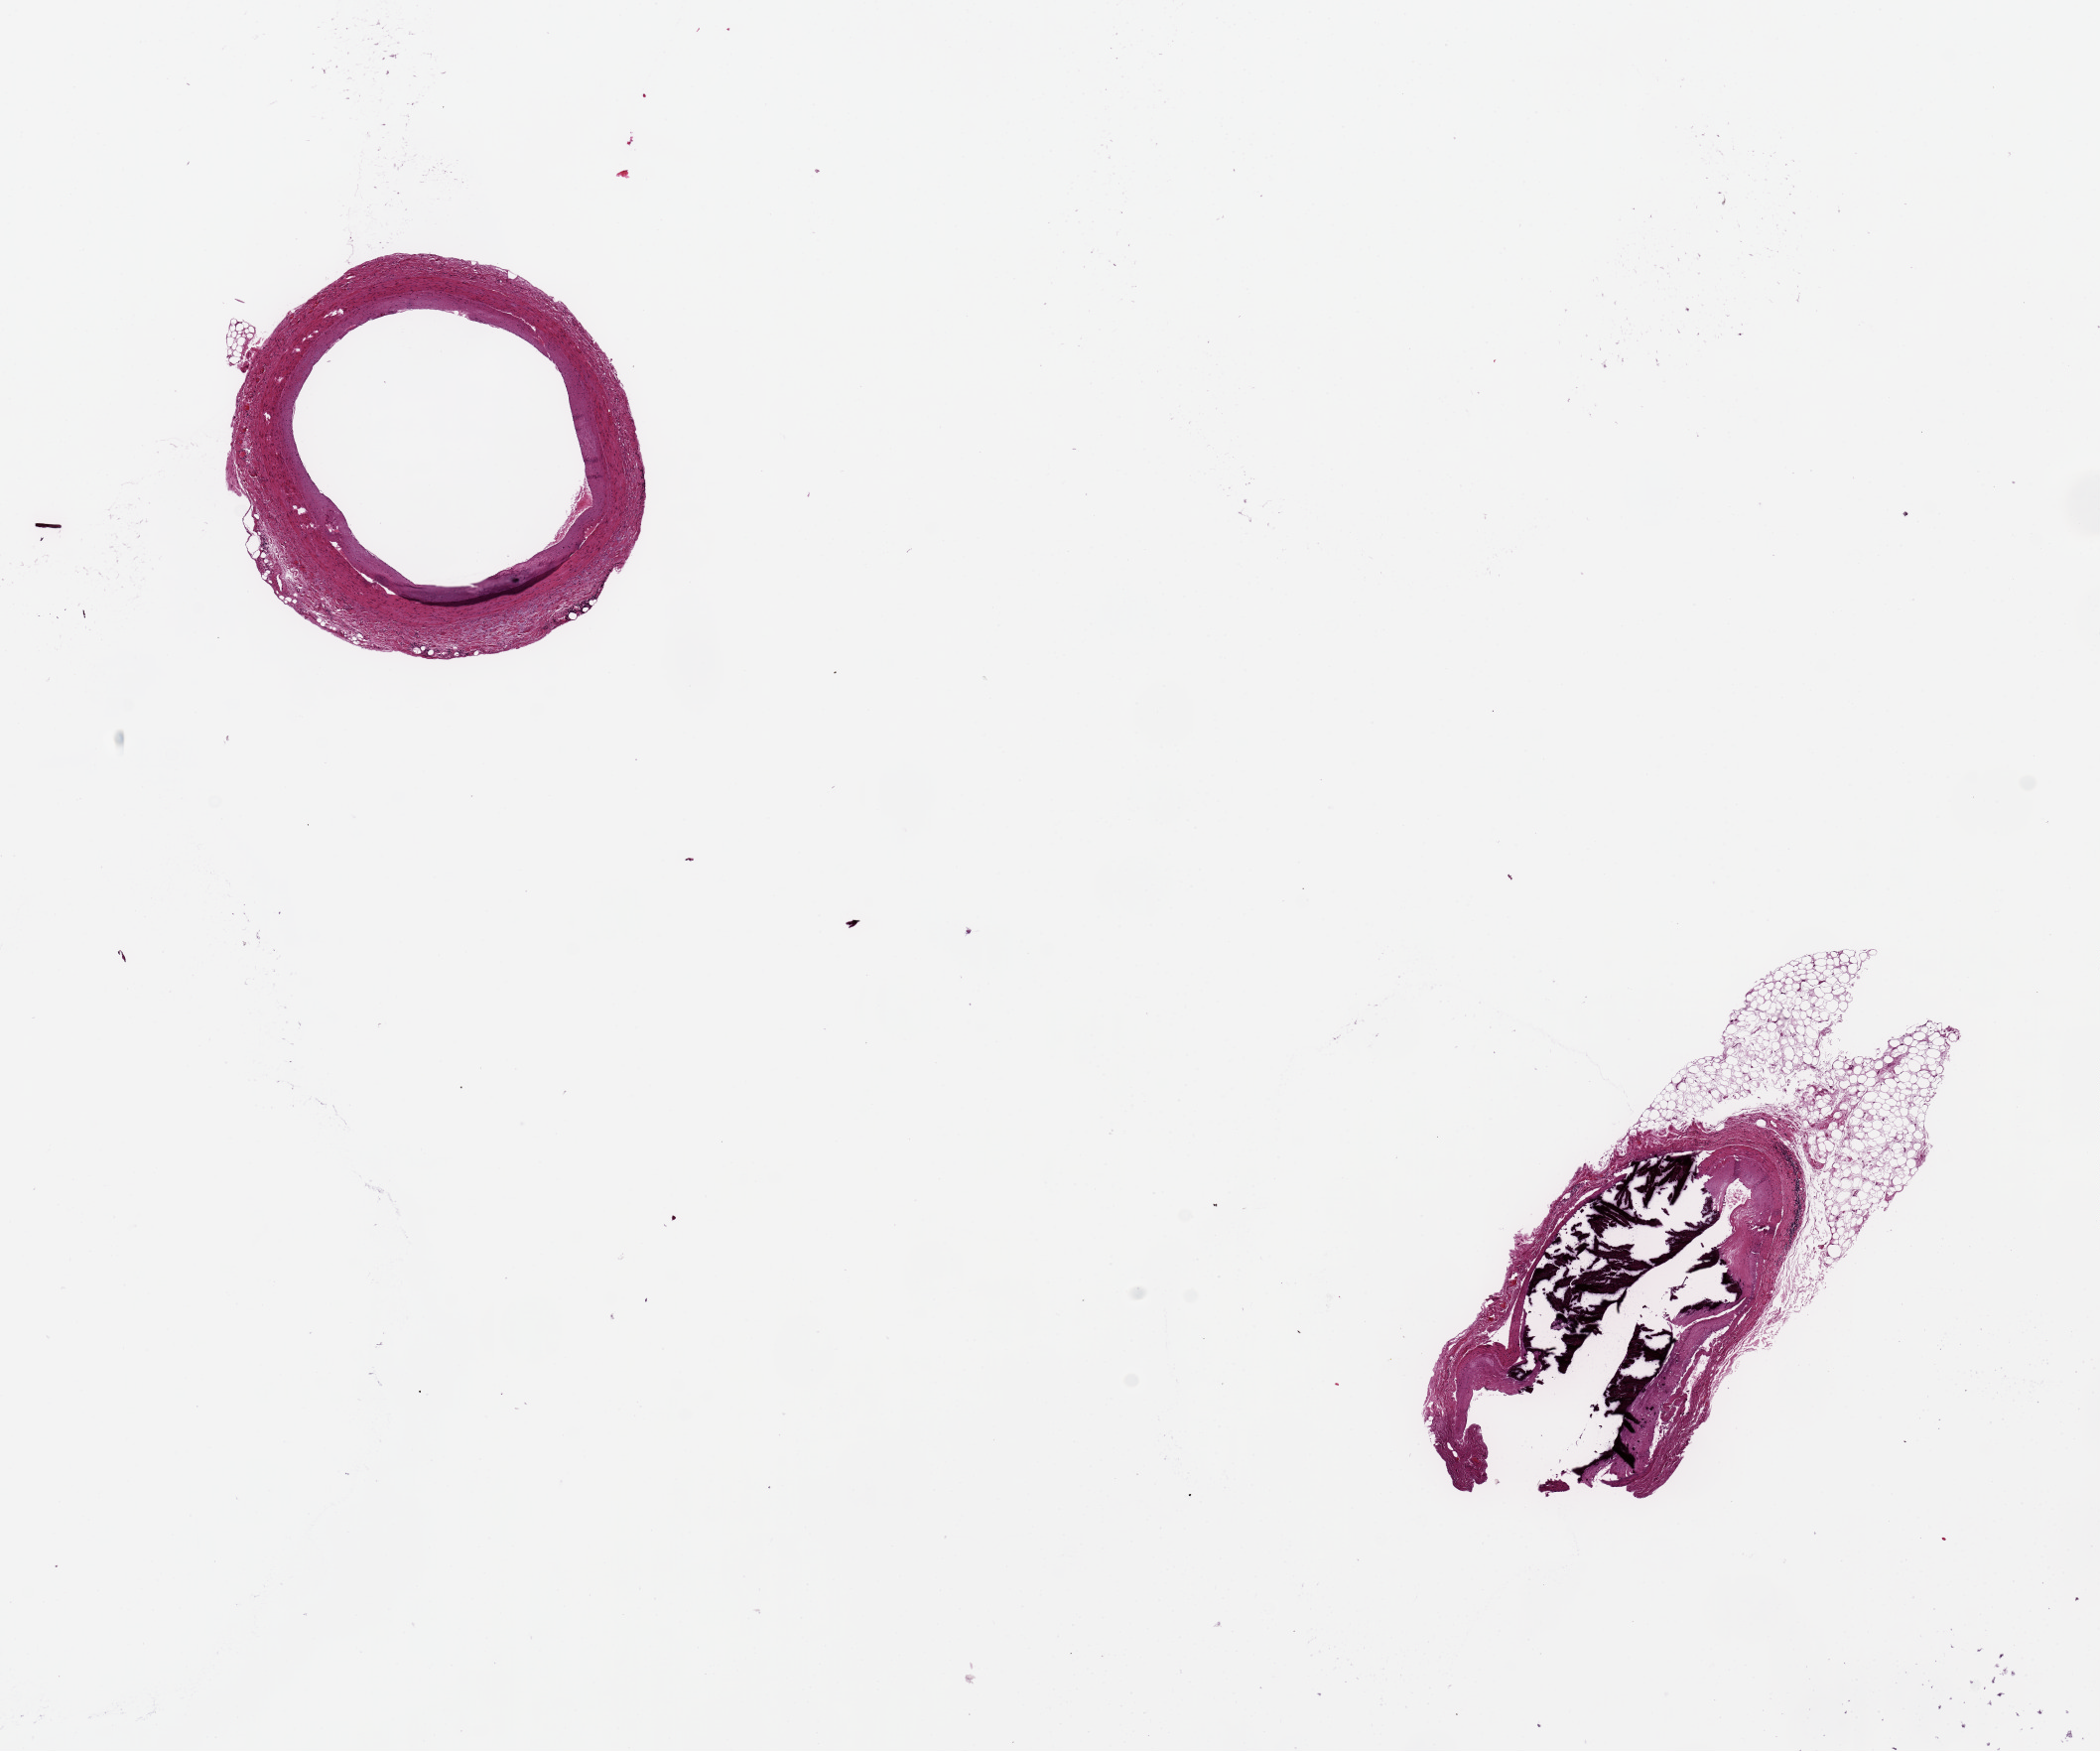
Whole-slide image, hematoxylin and eosin (H&E) stain, whole scanned area (about 16.7 x 14.0 mm, from a 20x scan) shown as a low-resolution overview, PAXgene-fixed paraffin-embedded (PFPE) section, section of coronary artery (target tissue), donor tissue sample.
Reviewer comment on this tissue sample: 2 ~3mm d. specimens, one with subtotally occlusive, calcified atherosclerosis.